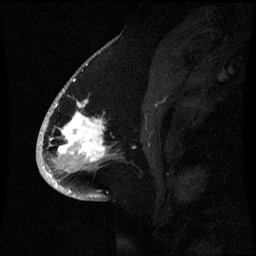
Breast MRI (dynamic contrast-enhanced), one sagittal slice. Position 34 of 60 along the scan axis. Dynamic contrast-enhanced series, image 2 of 3 at this slice position (ordered by acquisition). 1.5 T. TE 4.2 ms, TR 8.4 ms. 2.1 mm slice thickness. 256 × 256 image matrix, field of view 220 × 220 mm. Female patient, age 53 years. From the clinical record (not read from this slice): setting: breast cancer imaged before/during neoadjuvant chemotherapy; receptor status: HR-positive, HER2-negative.
Structures marked on this image (semi-automatic segmentation, software-assisted and operator-edited):
- analysis volume of interest (the breast-tissue region the enhancement analysis was run in; not a lesion): bounding box [x1, y1, x2, y2] px = [52, 90, 120, 171]
- tumour enhancement mask (voxels above the 70 % enhancement threshold inside the analysis volume of interest): [56, 92, 107, 161]